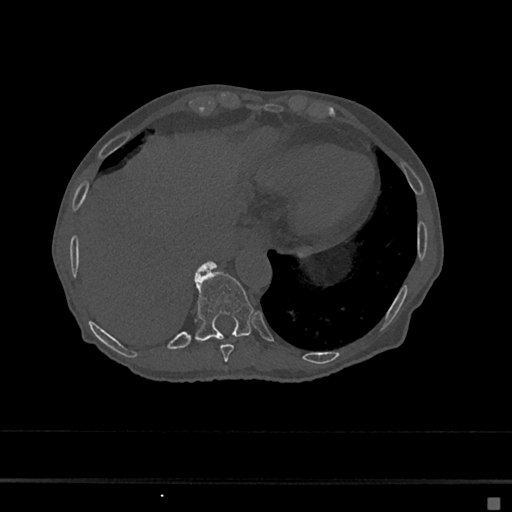
CT including the spine, one axial slice. Position 239 of 797 along the scan axis. Reconstruction kernel Br40s/3. 120 kVp. Bone window (W 1800 / L 400 HU). 0.5 mm slice thickness. 512 × 512 image matrix, field of view 360 × 360 mm. Female patient, age 68 years. Case-level facts recorded for this patient, not image findings: primary cancer: renal.
Annotated regions visible in this slice (semi-automatically segmented with operator editing):
- T10 vertebra: bounding box <195,264,254,341> (left, top, right, bottom; pixels)
- T11 vertebra: <196,263,212,275>
- T9 vertebra: <220,344,235,362>